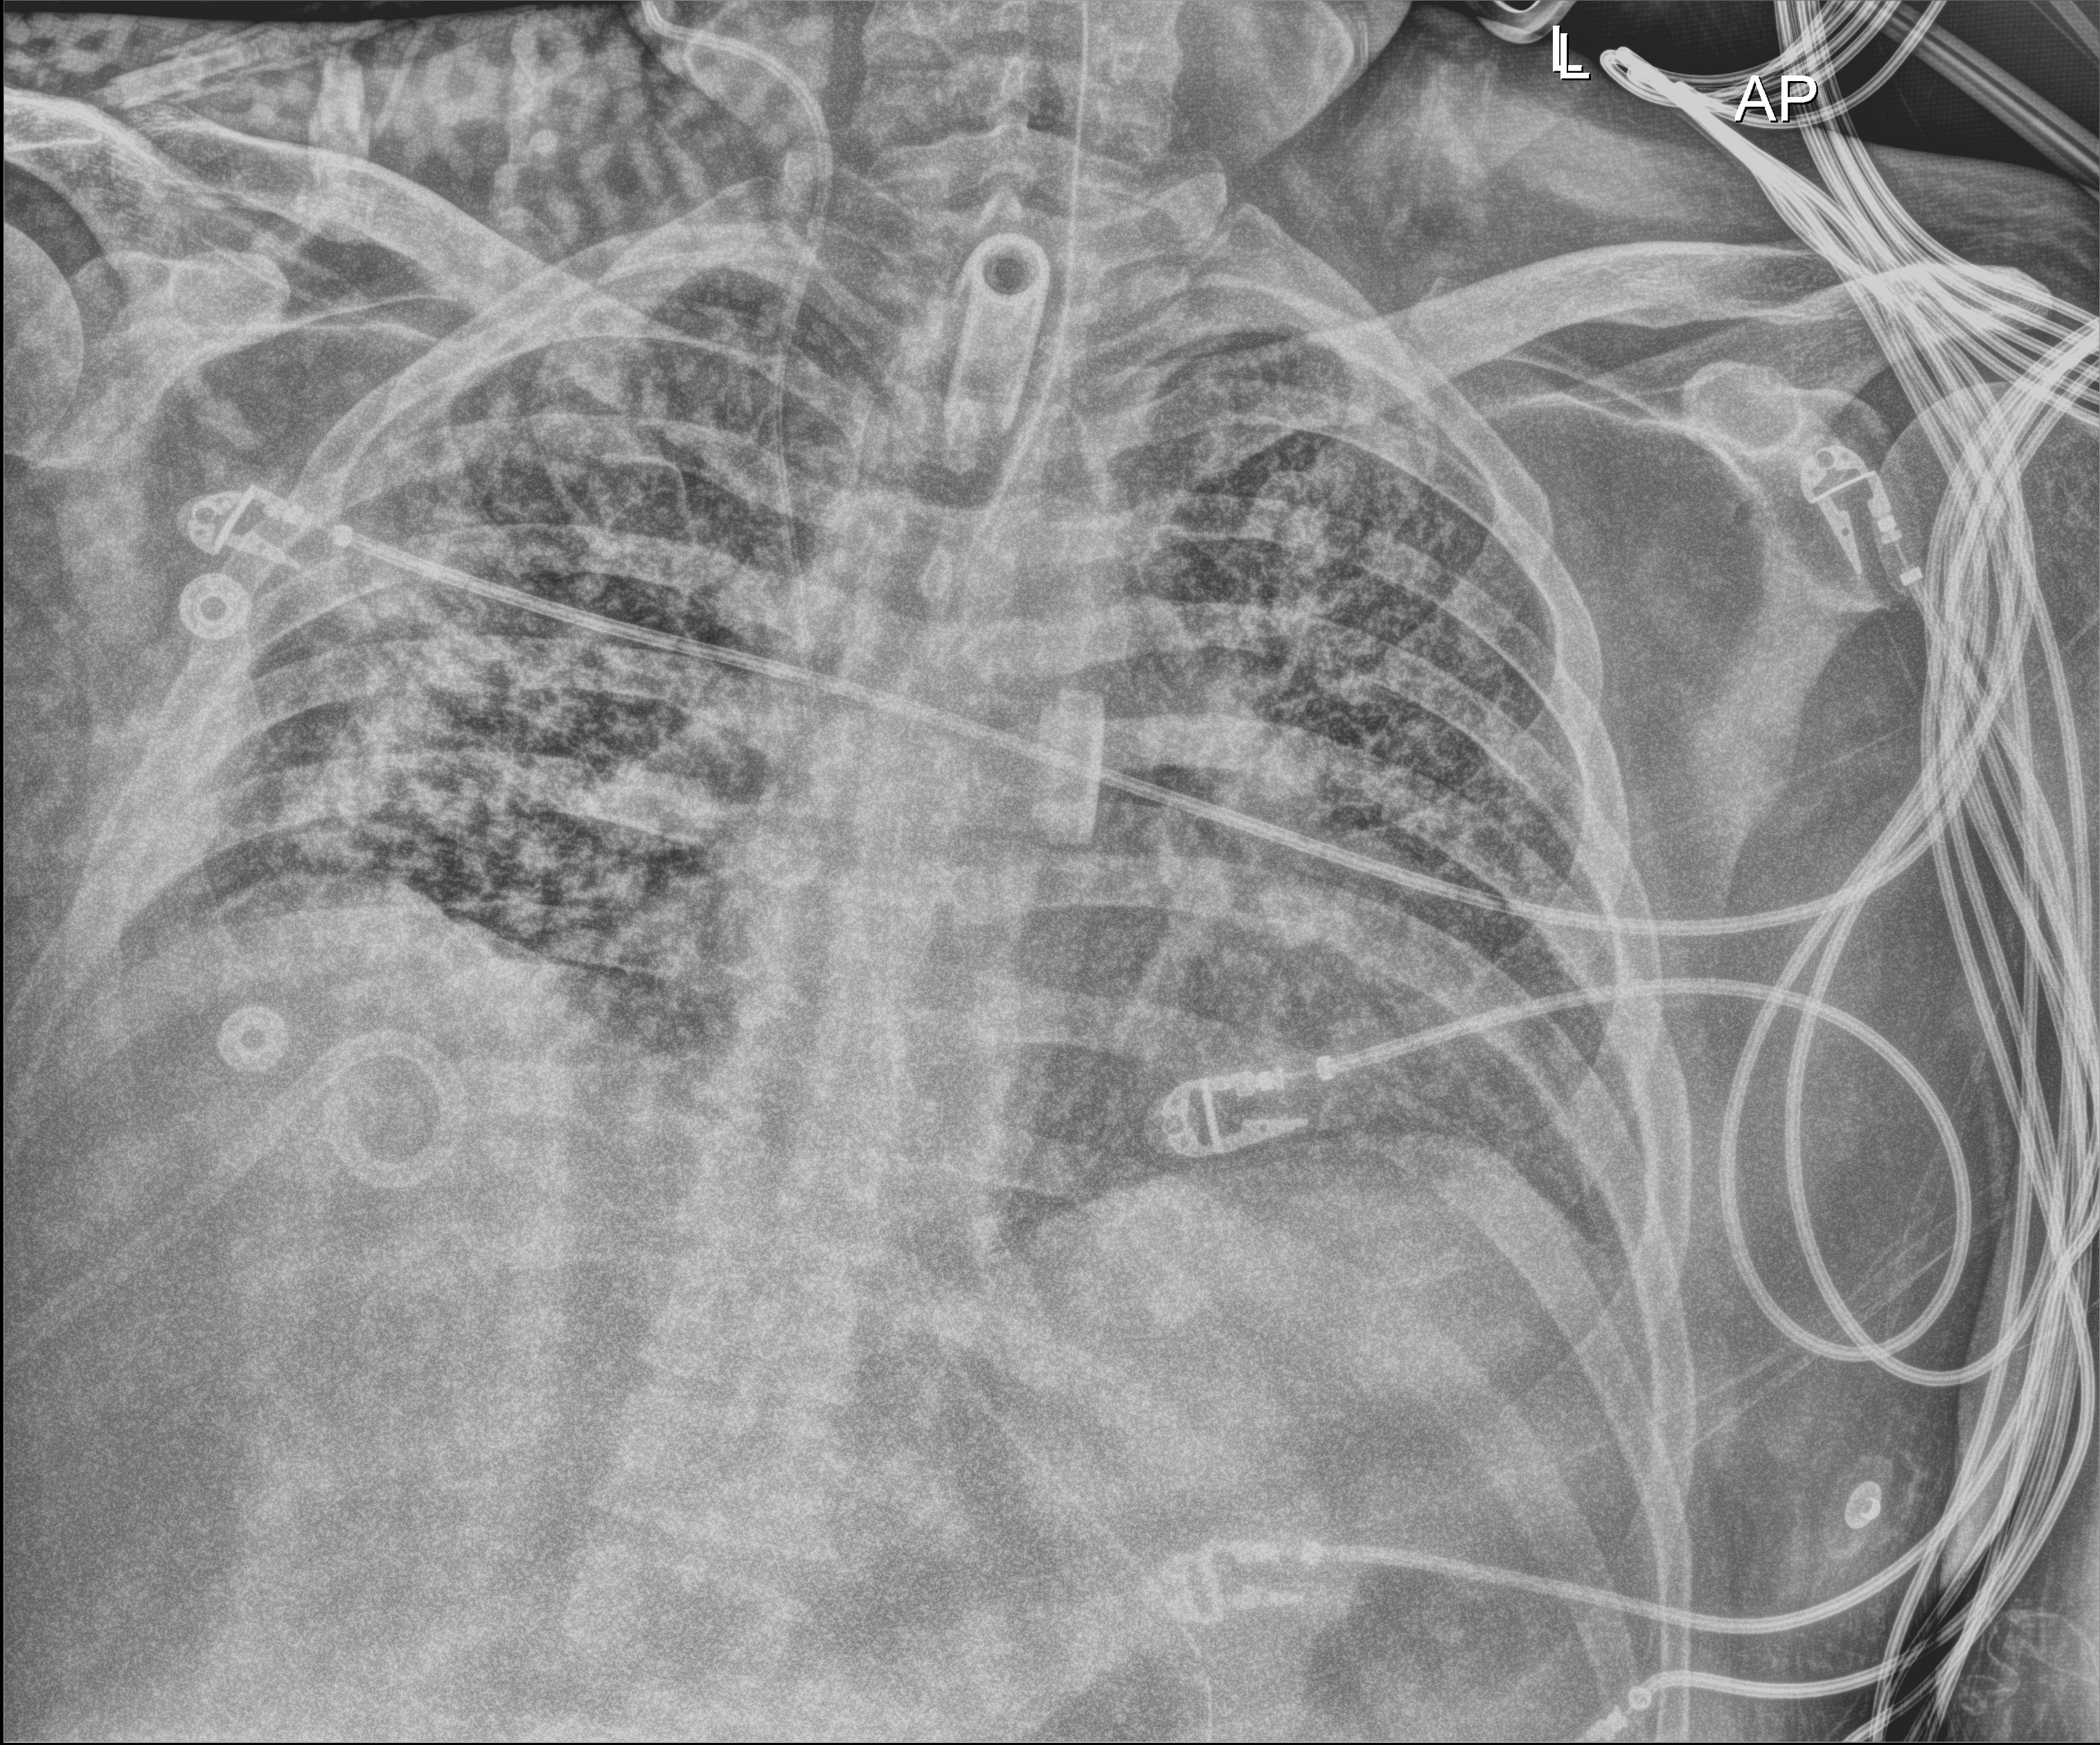
Bedside chest radiograph (digital radiography); anteroposterior (AP) projection. Patient hospitalised with COVID-19; male, aged 18–59 years.
From the hospital-stay record, not from the radiograph (when in the stay this image was taken is not recorded):
- admitted to intensive care during this hospital stay: yes